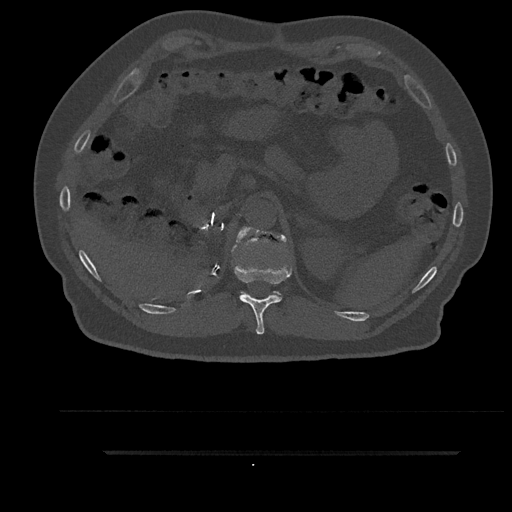
CT including the spine, one axial slice. Position 283 of 797 along the scan axis. 120 kVp. Bone window (W 1800 / L 400 HU). 0.5 mm slice thickness. 512 × 512 image matrix, field of view 432 × 432 mm. Patient: male, 63 years. Case-level facts recorded for this patient, not image findings: primary cancer: renal; vertebrae with lytic lesions (as recorded): T8.
Outlined on this slice (semi-automatically segmented with operator editing):
- T11 vertebra: box from (x=234, y=228) to (x=292, y=335) px
- T12 vertebra: (x=232, y=226)–(x=286, y=295)